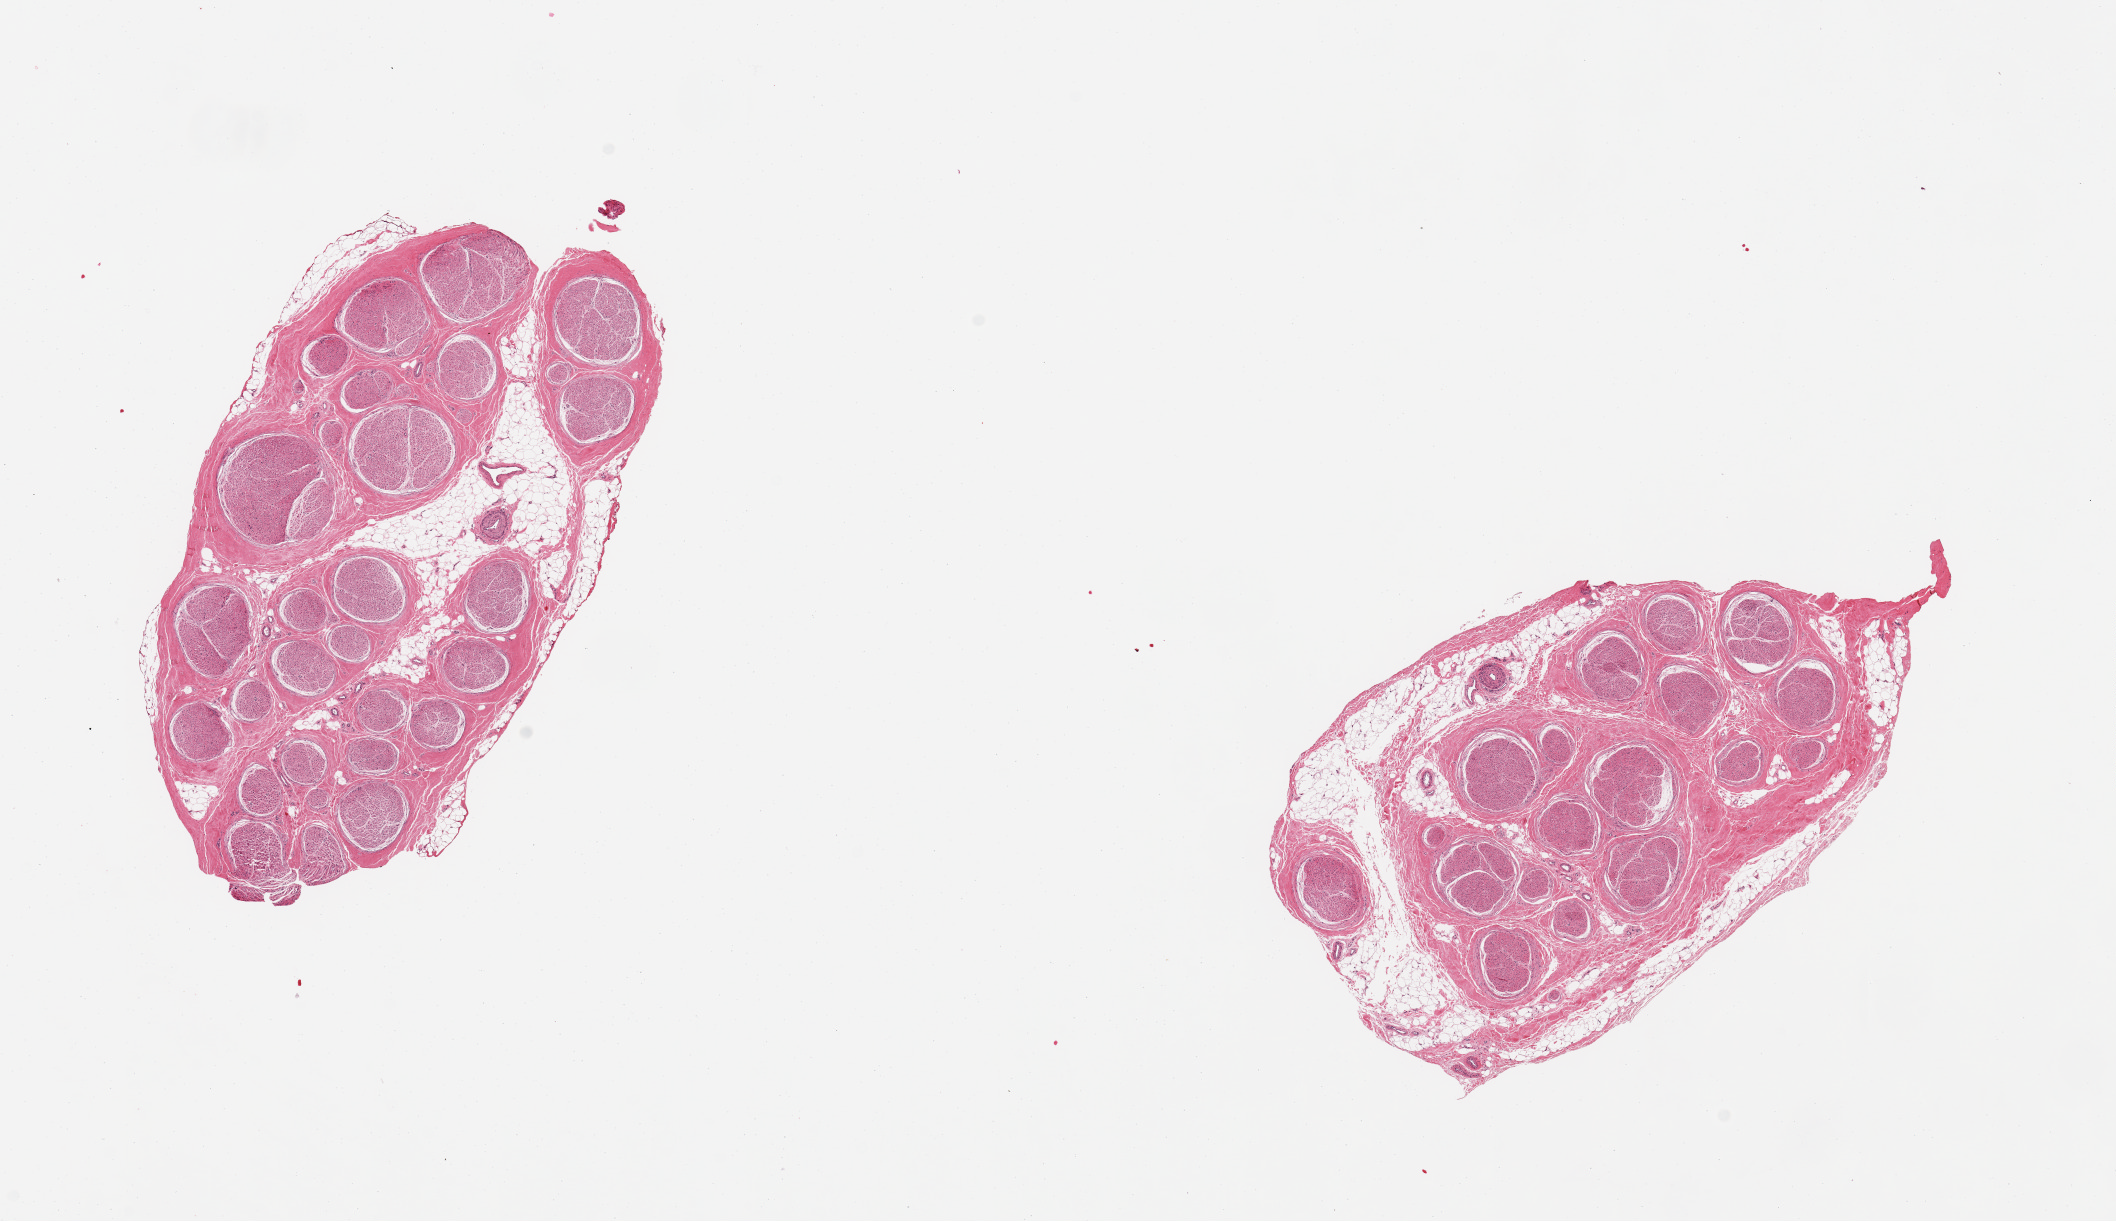
Digitized haematoxylin and eosin-stained section, low-resolution overview of the scanned area, about 16.7 x 9.7 mm; PAXgene-fixed paraffin-embedded (PFPE) section; sampled site (target tissue): tibial nerve; donor tissue sample. Donor: male.
Pathologist's review note for this sample: 2 pieces focal adherent fat up to ~0.5mm.